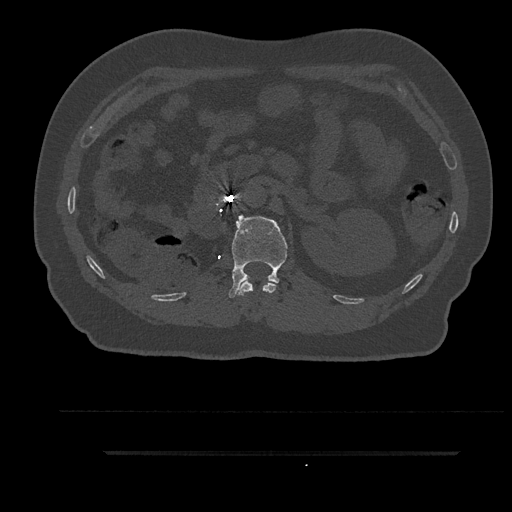
CT including the spine, one axial slice; position 194 of 797 along the scan axis; 120 kVp; bone window (W 1800 / L 400 HU); 0.5 mm slice thickness; 512 × 512 image matrix. Male patient, age 63 years. From the clinical record (not read from this slice): primary cancer: renal; vertebrae with lytic lesions (as recorded): T8.
Annotated regions visible in this slice (semi-automatically segmented with operator editing):
- L1 vertebra: box from (x=228, y=215) to (x=288, y=298) px
- T12 vertebra: (x=239, y=279)–(x=276, y=295)